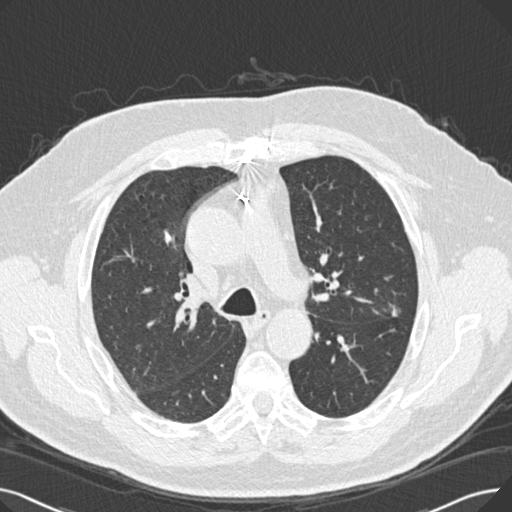
Low-dose screening chest CT, one axial slice; position 174 of 269 along the scan axis; 120 kVp; lung window (W 1500 / L -600 HU); 512 × 512 image matrix, field of view 370 × 370 mm.
Annotated regions visible in this slice (outlined manually by an expert reader):
- lesion 1 (tumor, upper lobe of left lung): bounding box [x1, y1, x2, y2] px = [391, 305, 398, 317]